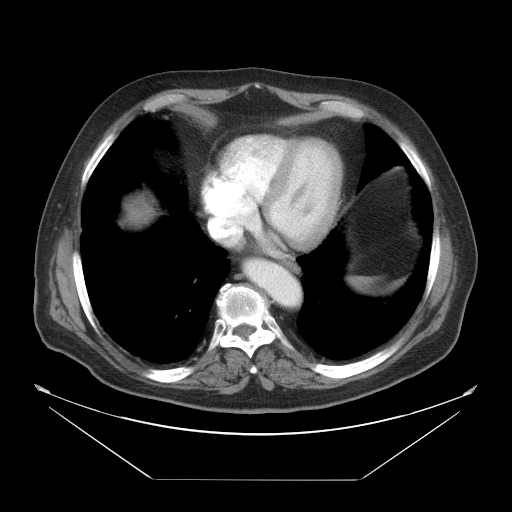
Contrast-enhanced abdominal CT, one axial slice. Slice 45 of 45 in the series (ordered by position). Reconstruction kernel STANDARD. Intravenous contrast given. Soft-tissue window (W 400 / L 40 HU). 5 mm slice thickness. 512 × 512 image matrix, field of view 463 × 463 mm. Male patient, age 87 years. From the clinical record (not read from this slice): diagnosis: colorectal cancer liver metastases, imaged before liver resection; multiple liver metastases: no; largest metastasis: 4.5 cm.
Annotated regions visible in this slice (outlined manually by an expert reader):
- liver: bounding box [x1, y1, x2, y2] px = [120, 186, 159, 230]